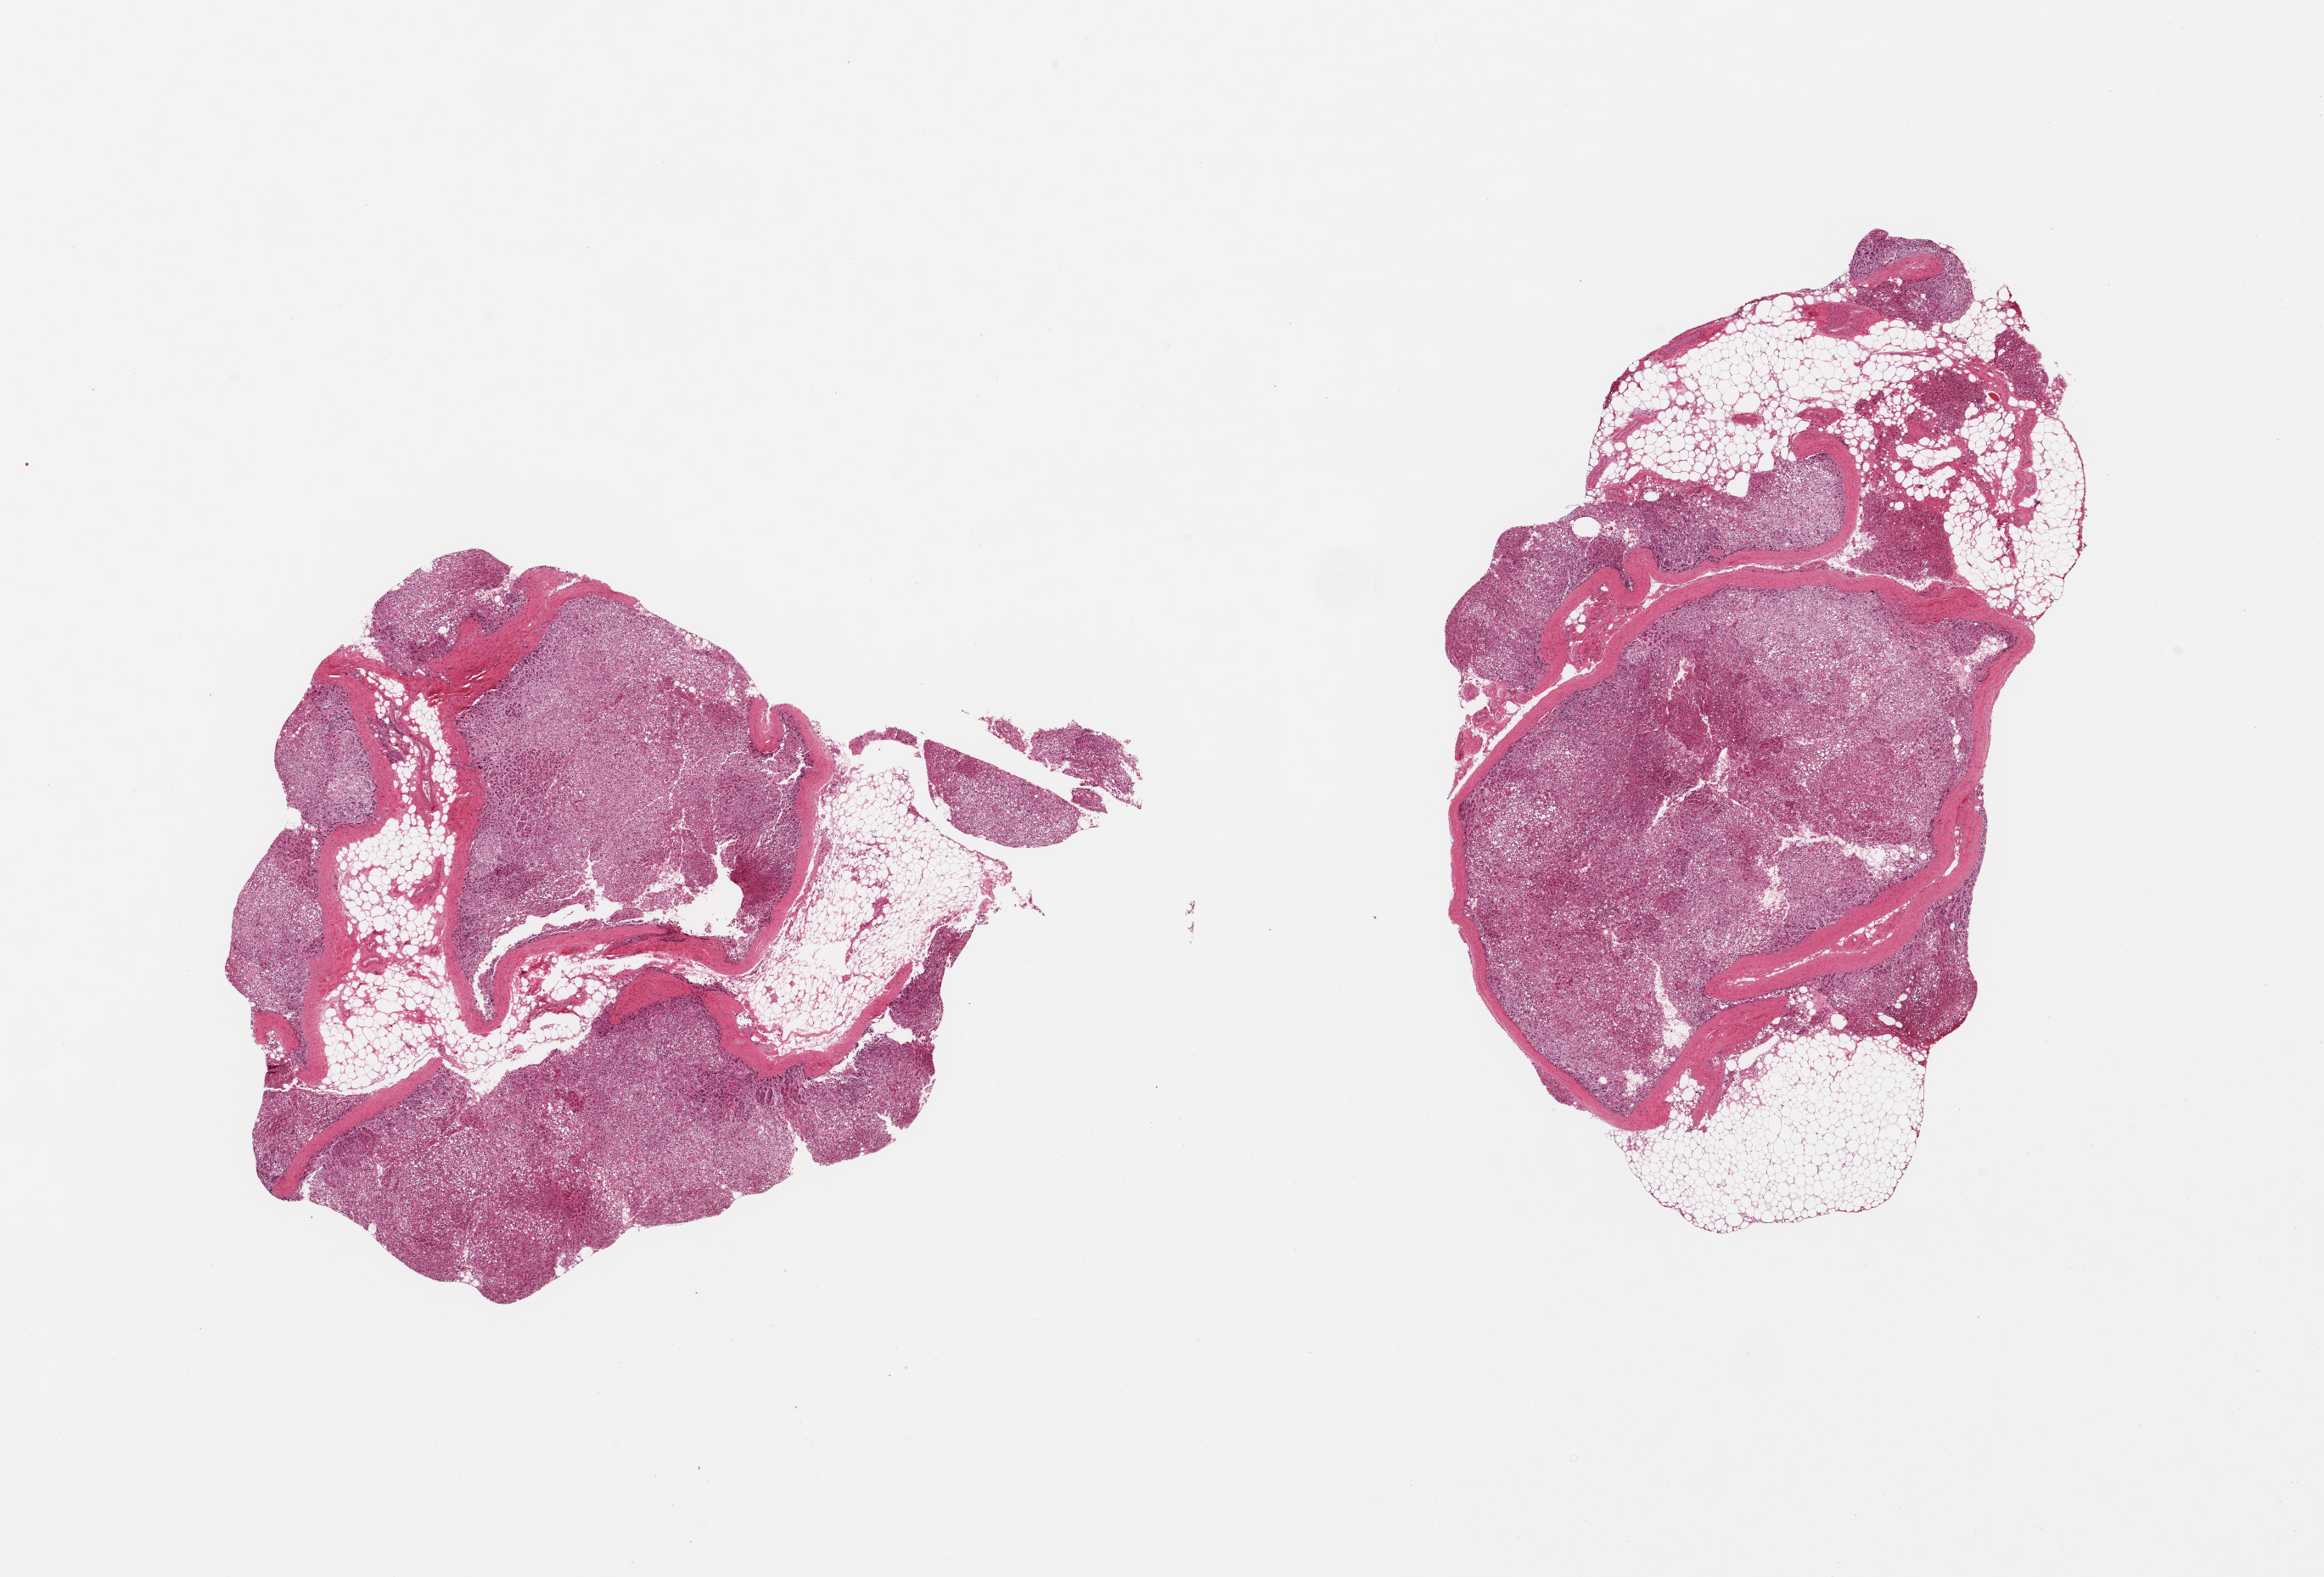
Digitized haematoxylin and eosin-stained section, brightfield, a low-resolution overview of the entire scanned area, about 21.7 x 14.7 mm. PAXgene-fixed, paraffin-embedded tissue. Target tissue: adrenal gland. Donor tissue sample. Male donor.
Reviewer comment on this tissue sample: 2 pieces; 30% fat in each.